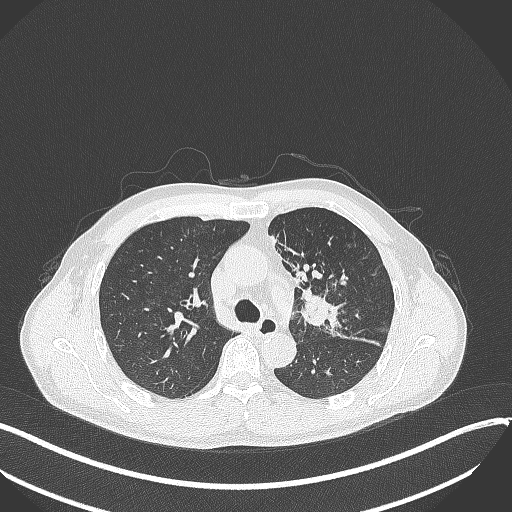
Chest CT, one axial slice; position 230 of 411 along the scan axis; reconstruction kernel B70f; 120 kVp; lung window (W 1500 / L -600 HU); 1 mm slice thickness; 512 × 512 image matrix, field of view 400 × 400 mm. Patient: male, 56 years. From the clinical record (not read from this slice): clinical TNM (as recorded): T2a N0 M0.
Outlined on this slice (rectangle marked by the reading radiologist):
- lung tumour (recorded histology: squamous cell carcinoma): box from (x=299, y=285) to (x=351, y=334) px